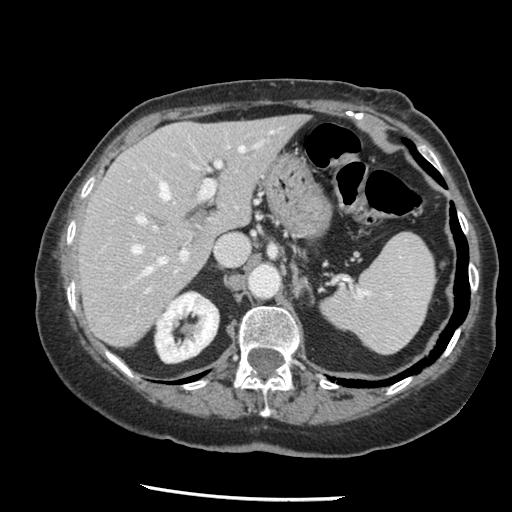
Contrast-enhanced abdominal CT, one axial slice. Slice 88 of 148 in the series (ordered by position). Reconstruction kernel STANDARD. 120 kVp. Intravenous contrast given. Soft-tissue window (W 400 / L 40 HU). 2.5 mm slice thickness. 512 × 512 image matrix. Female patient, age 85 years. From the clinical record (not read from this slice): diagnosis: colorectal cancer liver metastases, imaged before liver resection; multiple liver metastases: no; largest metastasis: 0.9 cm.
Annotated regions visible in this slice (manually delineated by an expert):
- hepatic veins: box from (x=132, y=147) to (x=243, y=274) px
- liver: (x=80, y=117)–(x=305, y=346)
- planned liver remnant (the part of the liver to remain after resection): (x=80, y=117)–(x=305, y=346)
- portal vein (with intrahepatic branches): (x=137, y=140)–(x=231, y=256)